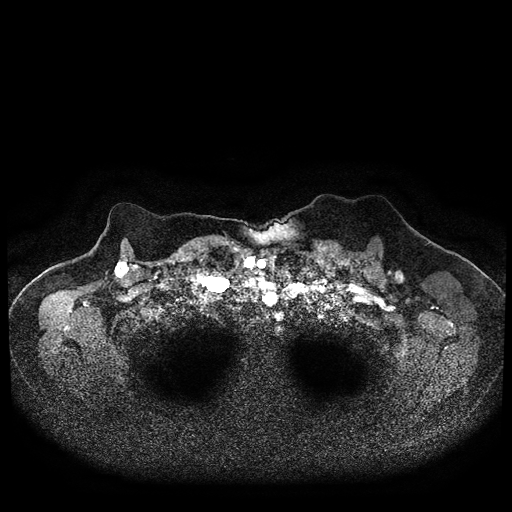
Breast MRI (dynamic contrast-enhanced, multi-phase), one axial slice. Position 84 of 116 along the scan axis. Dynamic contrast-enhanced series, time point 2 of 5 at this slice position (early post-contrast). 1.5 T. TE 2.7 ms, TR 5.4 ms. 2 mm slice thickness. 512 × 512 image matrix. Female patient, age 72 years.
Annotated regions visible in this slice (semi-automatic segmentation, software-assisted and operator-edited):
- breast lesion (labelled 'tumour' in the annotation; benign lesions carry a separate 'benign' label): bounding box [x1, y1, x2, y2] px = [114, 259, 131, 280]